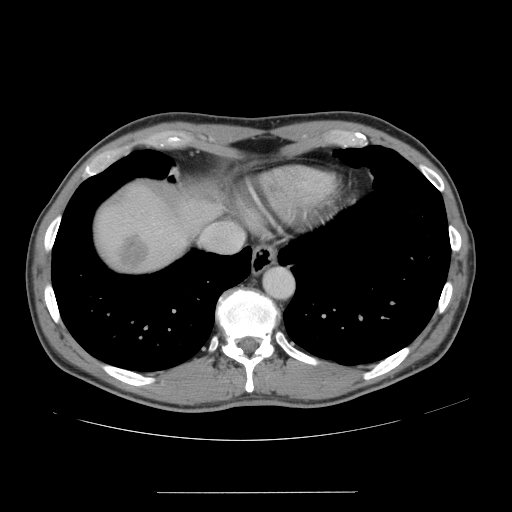
Contrast-enhanced abdominal CT, one axial slice; position 139 of 178 along the scan axis; 120 kVp; soft-tissue window (W 400 / L 40 HU); 2.5 mm slice thickness; 512 × 512 image matrix, field of view 401 × 401 mm. Male patient, age 53 years. From the clinical record (not read from this slice): diagnosis: colorectal cancer liver metastases, imaged before liver resection; multiple liver metastases: yes; largest metastasis: 2.4 cm; disease in both lobes: no.
Structures marked on this image (expert manual segmentation):
- liver: bounding box [x1, y1, x2, y2] px = [95, 184, 220, 272]
- planned liver remnant (the part of the liver to remain after resection): [205, 199, 220, 212]
- liver metastasis: [119, 236, 148, 268]